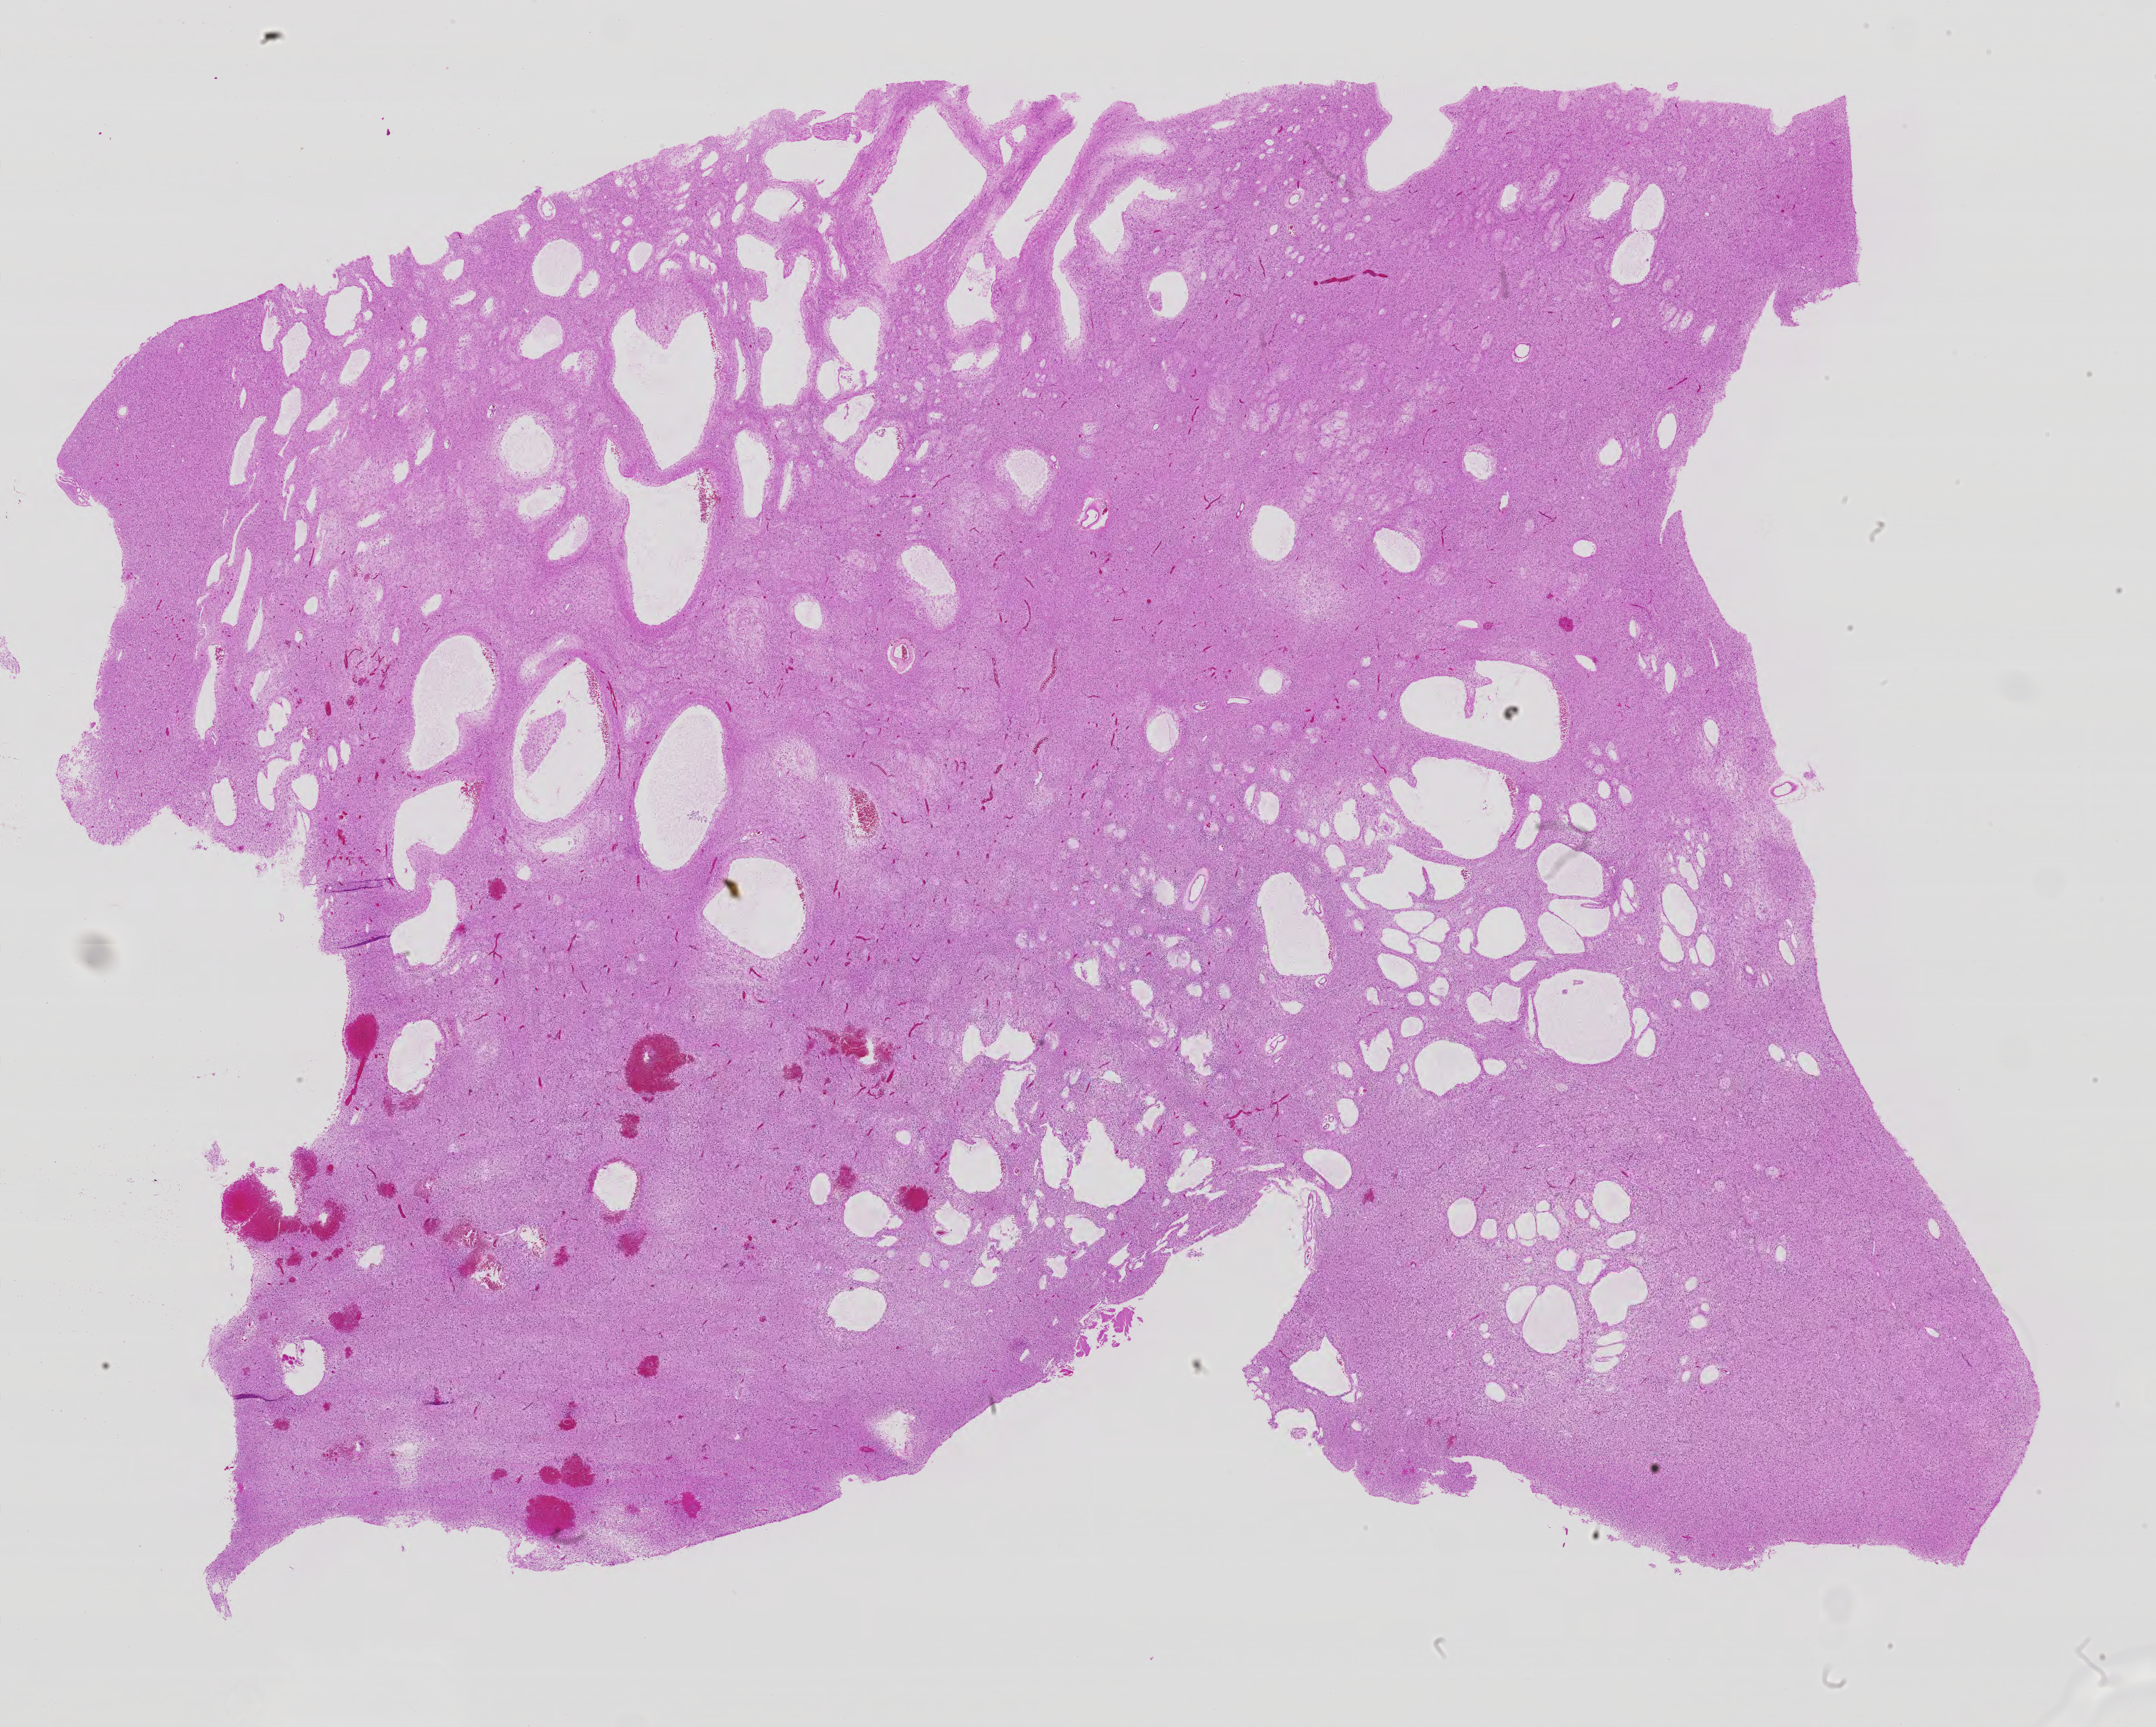
H&E-stained whole-slide image, shown as a low-resolution overview of the whole scanned area (about 24.3 x 19.4 mm, from a 40x scan); FFPE section; brain, primary tumour sample. Female, age 41 years at initial diagnosis.
Pathologic diagnosis: Astrocytoma, NOS (cerebrum).